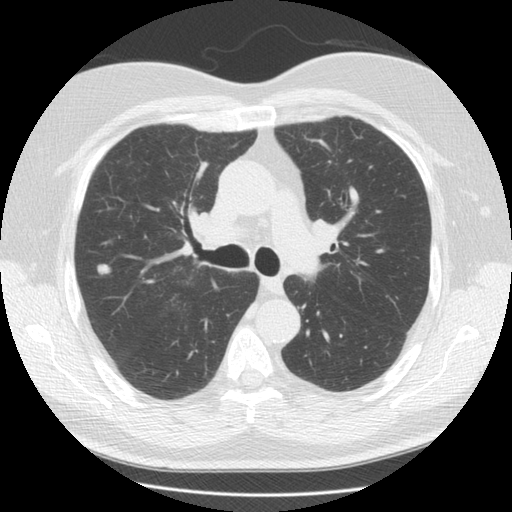
Low-dose screening chest CT, one axial slice; slice 92 of 146 in the series (ordered by position); reconstruction kernel STANDARD; lung window (W 1500 / L -600 HU); 512 × 512 image matrix, field of view 350 × 350 mm.
Structures marked on this image (expert manual segmentation):
- lesion 1 (tumor, upper lobe of right lung): bounding box (x1, y1, x2, y2) in pixels: (97, 263, 113, 275)